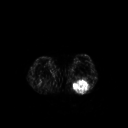
FDG PET of an extremity soft-tissue mass (from a PET/CT study), one axial slice. Slice 184 of 267 in the series (ordered by position). 3.27 mm slice thickness. 128 × 128 image matrix, field of view 500 × 500 mm. Male patient, age 54 years. Case-level facts recorded for this patient, not image findings: histological type: synovial sarcoma; site of the primary tumour: left poplietal fossa.
Annotated regions visible in this slice (expert contour drawn on MRI and transferred to this co-registered scan by the dataset authors):
- gross tumour volume (mass): bounding box <72,80,91,94> (left, top, right, bottom; pixels)